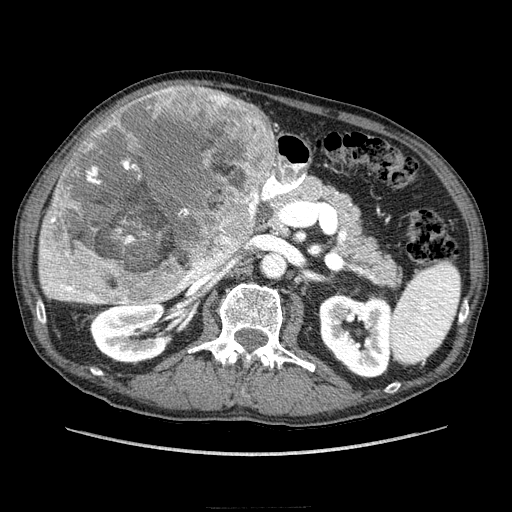
Contrast-enhanced abdominal CT (liver protocol), one axial slice. Position 119 of 218 along the scan axis. Soft-tissue window (W 400 / L 40 HU). 2.5 mm slice thickness. 512 × 512 image matrix. Case-level facts recorded for this patient, not image findings: diagnosis: hepatocellular carcinoma (patient treated with transarterial chemoembolisation; whether this scan precedes or follows treatment is not stated here); TNM stage (as recorded): Stage-IIIA.
Annotated regions visible in this slice (semi-automatically segmented with operator editing):
- liver parenchyma outside the tumour (the mass and vessels are separate outlines, so this box may not span the whole liver): bounding box <38,88,284,304> (left, top, right, bottom; pixels)
- mass: <43,81,276,306>
- liver vessels: <50,282,98,302>